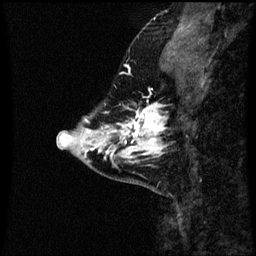
Breast MRI (dynamic contrast-enhanced), one sagittal slice. Dynamic contrast-enhanced series, image 2 of 3 at this slice position (ordered by acquisition). 1.5 T. TE 4.2 ms, TR 8.9 ms. 2 mm slice thickness. 256 × 256 image matrix, field of view 200 × 200 mm. Patient: female, 43 years. Case-level facts recorded for this patient, not image findings: setting: breast cancer imaged before/during neoadjuvant chemotherapy; receptor status: HR-positive, HER2-negative.
Structures marked on this image (semi-automatically segmented with operator editing):
- analysis volume of interest (the breast-tissue region the enhancement analysis was run in; not a lesion): bounding box (x1, y1, x2, y2) in pixels: (110, 102, 165, 163)
- tumour enhancement mask (voxels above the 70 % enhancement threshold inside the analysis volume of interest): (110, 104, 165, 159)